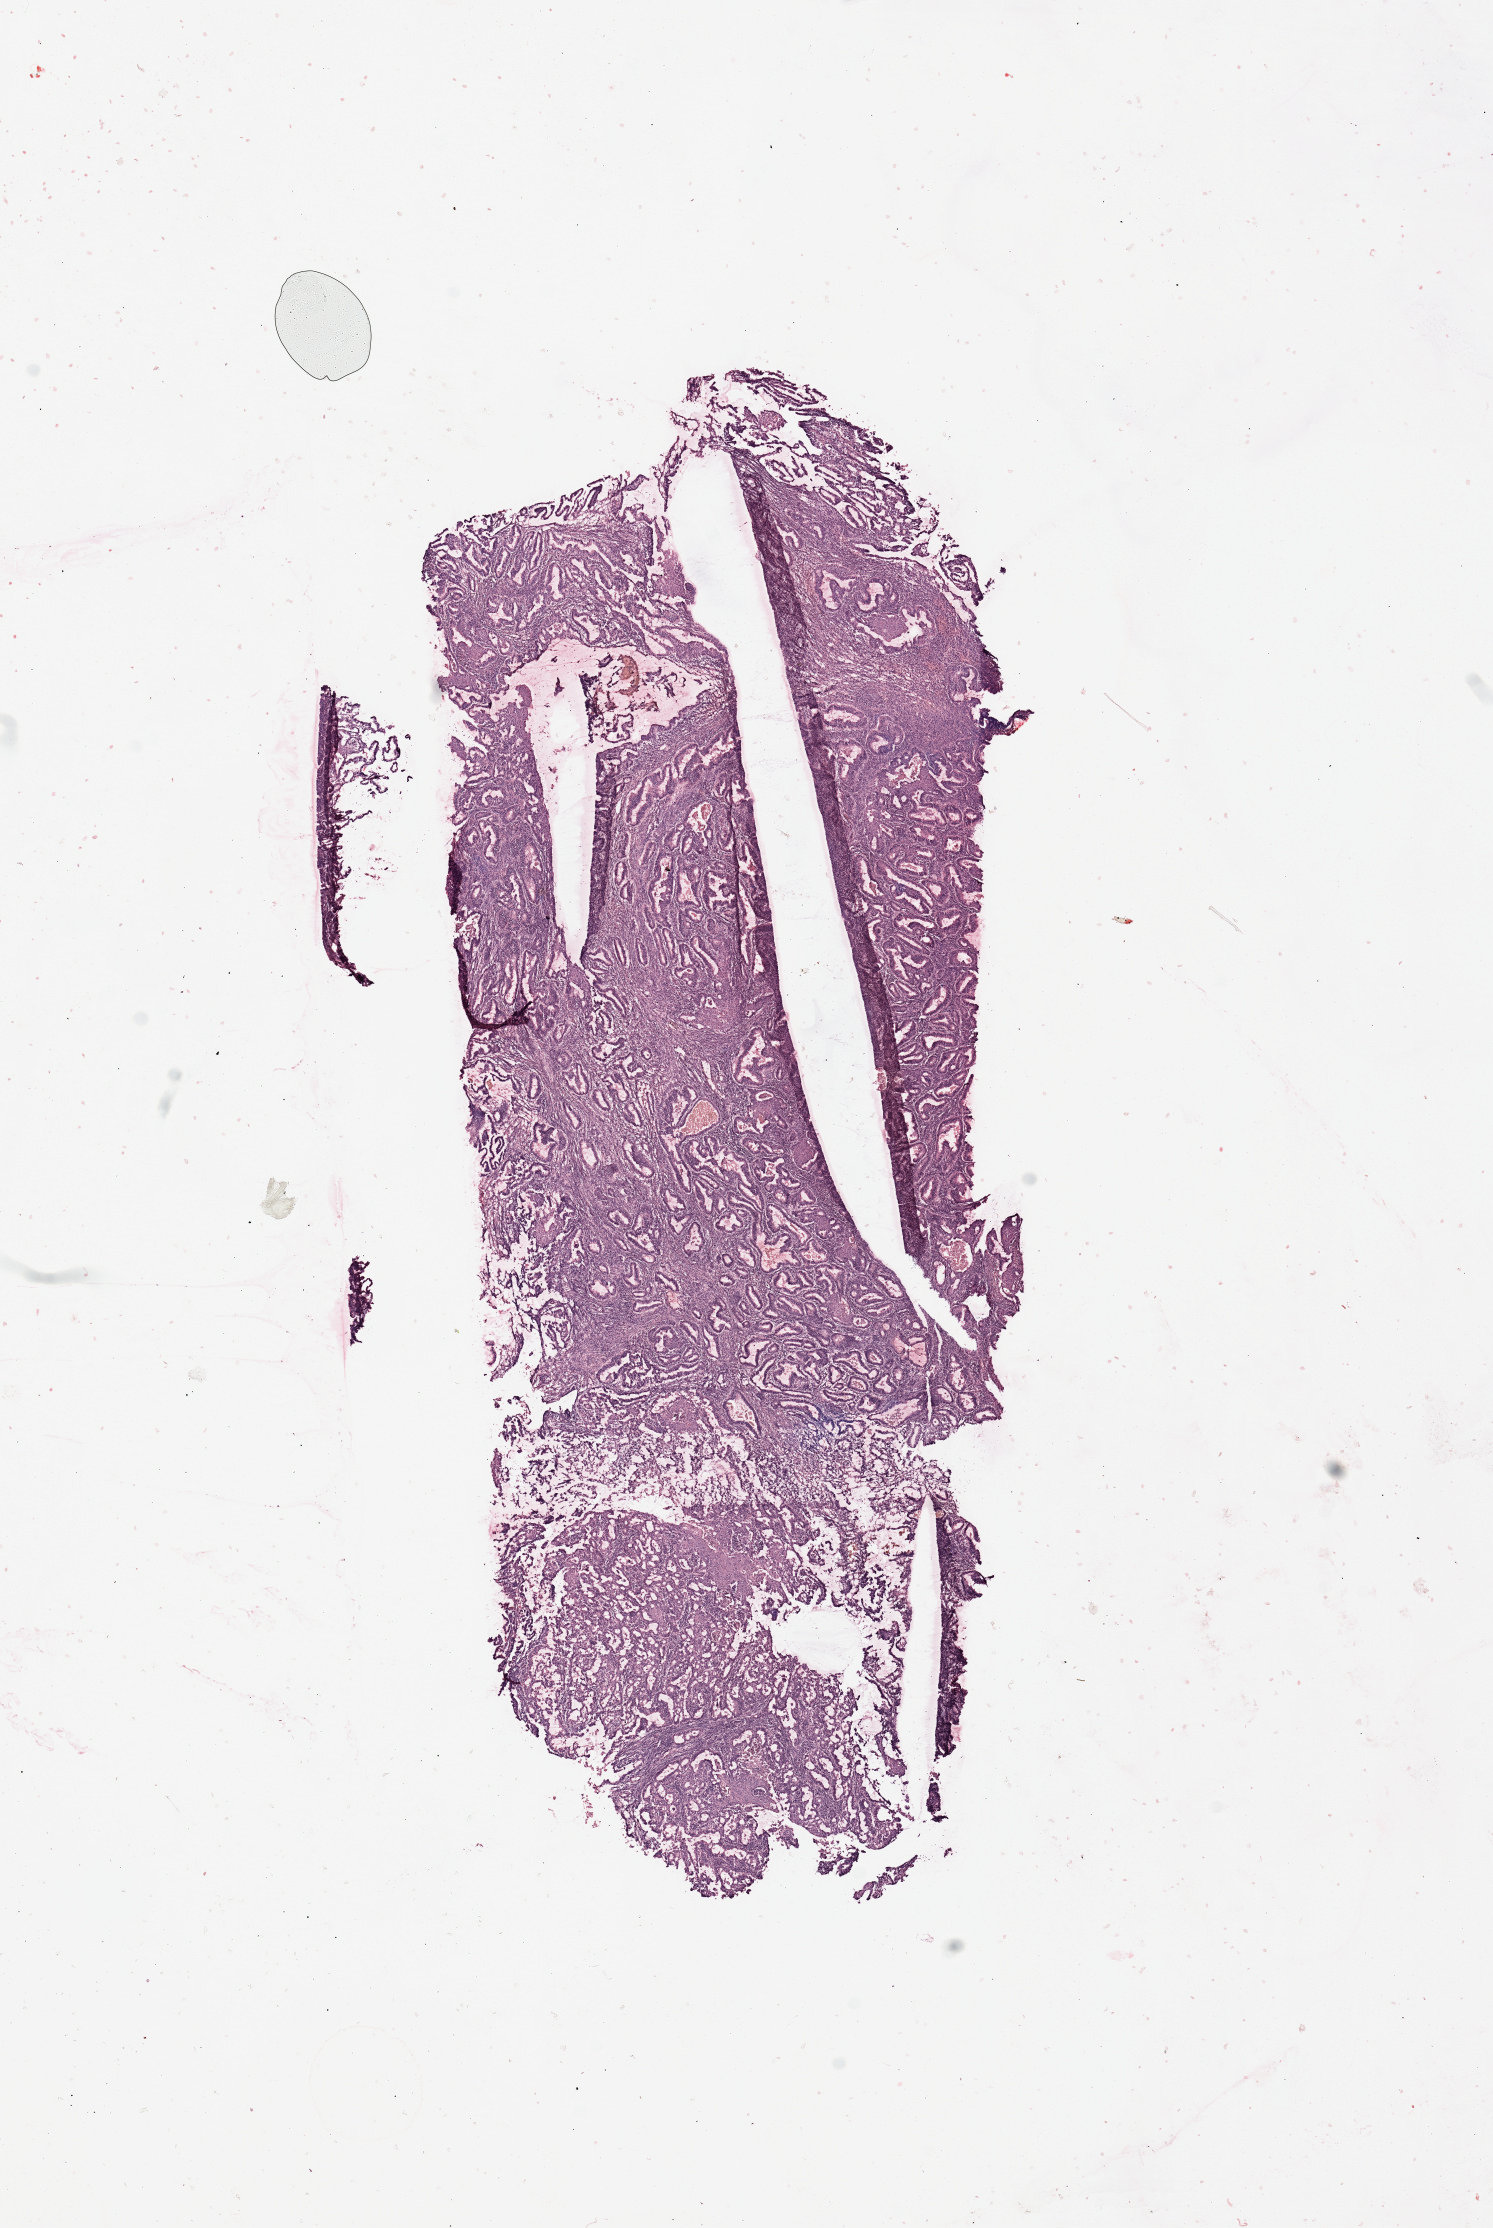
Whole-slide histology image, H&E — low-resolution overview of the scanned area, about 11.8 x 17.6 mm (acquisition: 20x scan); tumour tissue sample, sampled site: uterus. Female, 44 y/o. Histologic grade: G1 (well differentiated). Slide review estimates, as recorded: tumour nuclei 80%, necrosis 0%.
Histologic diagnosis: Endometrioid adenocarcinoma, NOS. AJCC pathologic stage: I.